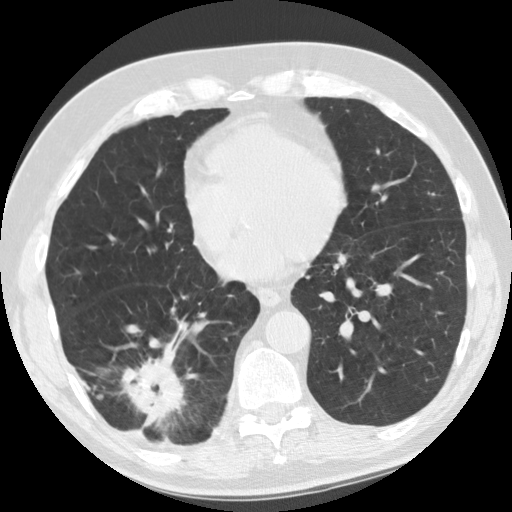
Low-dose screening chest CT, one axial slice; position 46 of 135 along the scan axis; reconstruction kernel STANDARD; 120 kVp; lung window (W 1500 / L -600 HU); 2.5 mm slice thickness; 512 × 512 image matrix, field of view 340 × 340 mm.
Annotated regions visible in this slice (expert manual segmentation):
- lesion 1 (tumor, lower lobe of right lung): bounding box [x1, y1, x2, y2] px = [120, 338, 187, 433]